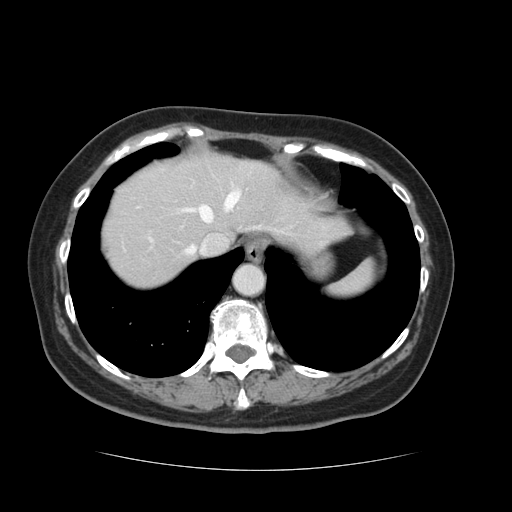
Contrast-enhanced abdominal CT, one axial slice; position 108 of 128 along the scan axis; 120 kVp; soft-tissue window (W 400 / L 40 HU); 2.5 mm slice thickness; 512 × 512 image matrix, field of view 366 × 366 mm. Female patient, age 67 years. Case-level facts recorded for this patient, not image findings: diagnosis: colorectal cancer liver metastases, imaged before liver resection; multiple liver metastases: yes; largest metastasis: 3 cm; chemotherapy before resection: no.
Annotated regions visible in this slice (expert manual segmentation):
- hepatic veins: bounding box (x1, y1, x2, y2) in pixels: (184, 190, 284, 256)
- liver: (100, 154, 341, 291)
- planned liver remnant (the part of the liver to remain after resection): (100, 158, 342, 290)